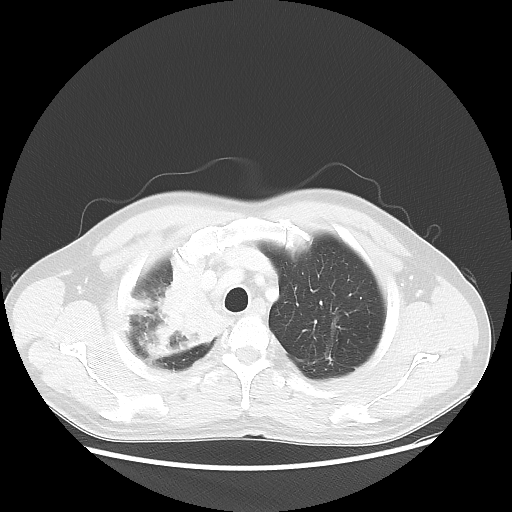
Chest CT, one axial slice. Position 45 of 56 along the scan axis. Lung window (W 1500 / L -600 HU). 5 mm slice thickness. 512 × 512 image matrix. Patient: male, 60 years. Case-level facts recorded for this patient, not image findings: clinical TNM (as recorded): T2a N1 M0.
Structures marked on this image (bounding box drawn by a radiologist):
- lung tumour (recorded histology: squamous cell carcinoma): bounding box (x1, y1, x2, y2) in pixels: (132, 251, 243, 377)